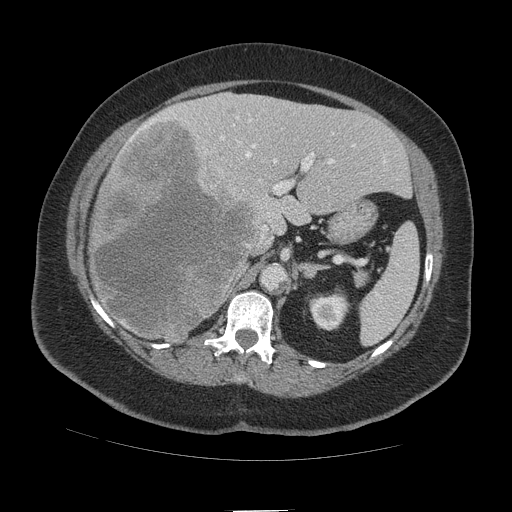
Contrast-enhanced abdominal CT (liver protocol), one axial slice. Position 63 of 109 along the scan axis. 140 kVp. Soft-tissue window (W 400 / L 40 HU). 512 × 512 image matrix. From the clinical record (not read from this slice): diagnosis: hepatocellular carcinoma (patient treated with transarterial chemoembolisation; whether this scan precedes or follows treatment is not stated here); TNM stage (as recorded): Stage-IVB; Child-Pugh class: A; tumour differentiation: poorly differentiated.
Outlined on this slice (semi-automatic segmentation, software-assisted and operator-edited):
- liver parenchyma outside the tumour (the mass and vessels are separate outlines, so this box may not span the whole liver): bounding box (x1, y1, x2, y2) in pixels: (90, 92, 410, 340)
- mass: (88, 116, 258, 343)
- liver vessels: (130, 110, 386, 239)